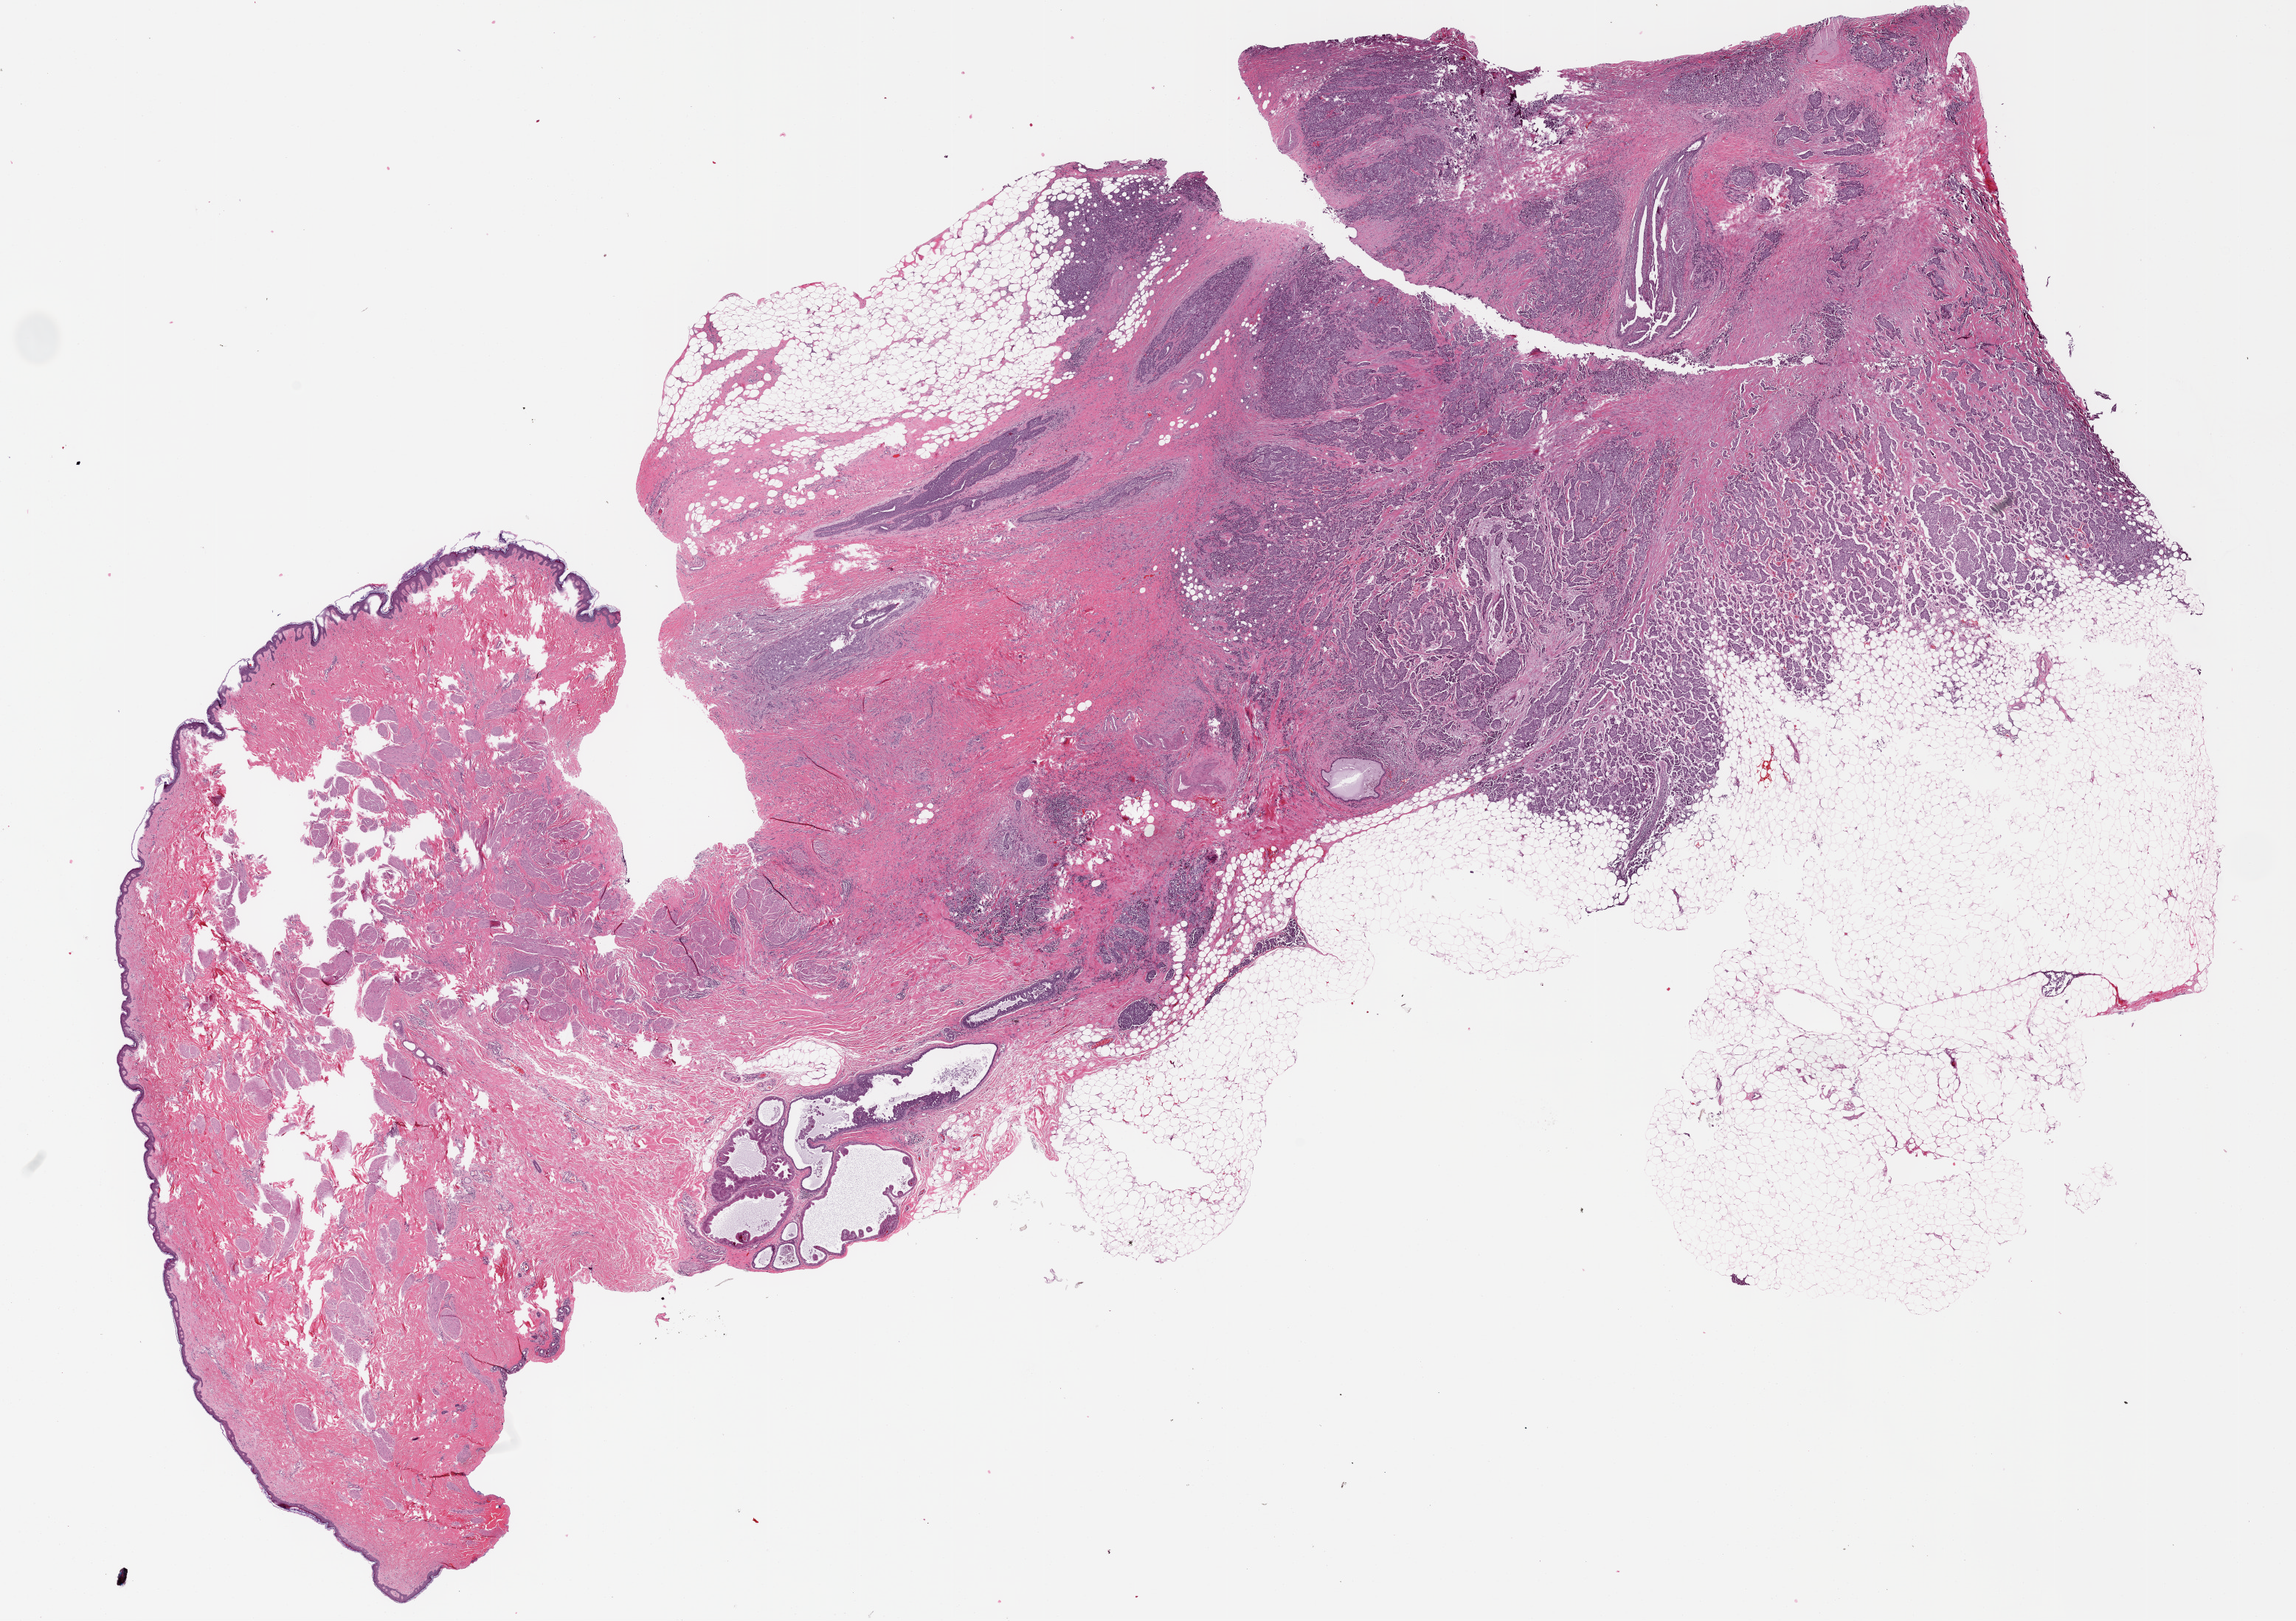
H&E whole-slide image — a low-resolution overview of the entire scanned area, about 24.9 x 17.6 mm (slide scanned at 20x), formalin-fixed paraffin-embedded (FFPE) diagnostic section, primary tumour sample from the breast. Patient: female, age at initial diagnosis 71 years.
• AJCC pathologic stage: IIB
• lymph nodes positive (case pathology): 3 of 11 examined
• pathologic diagnosis: Infiltrating duct mixed with other types of carcinoma